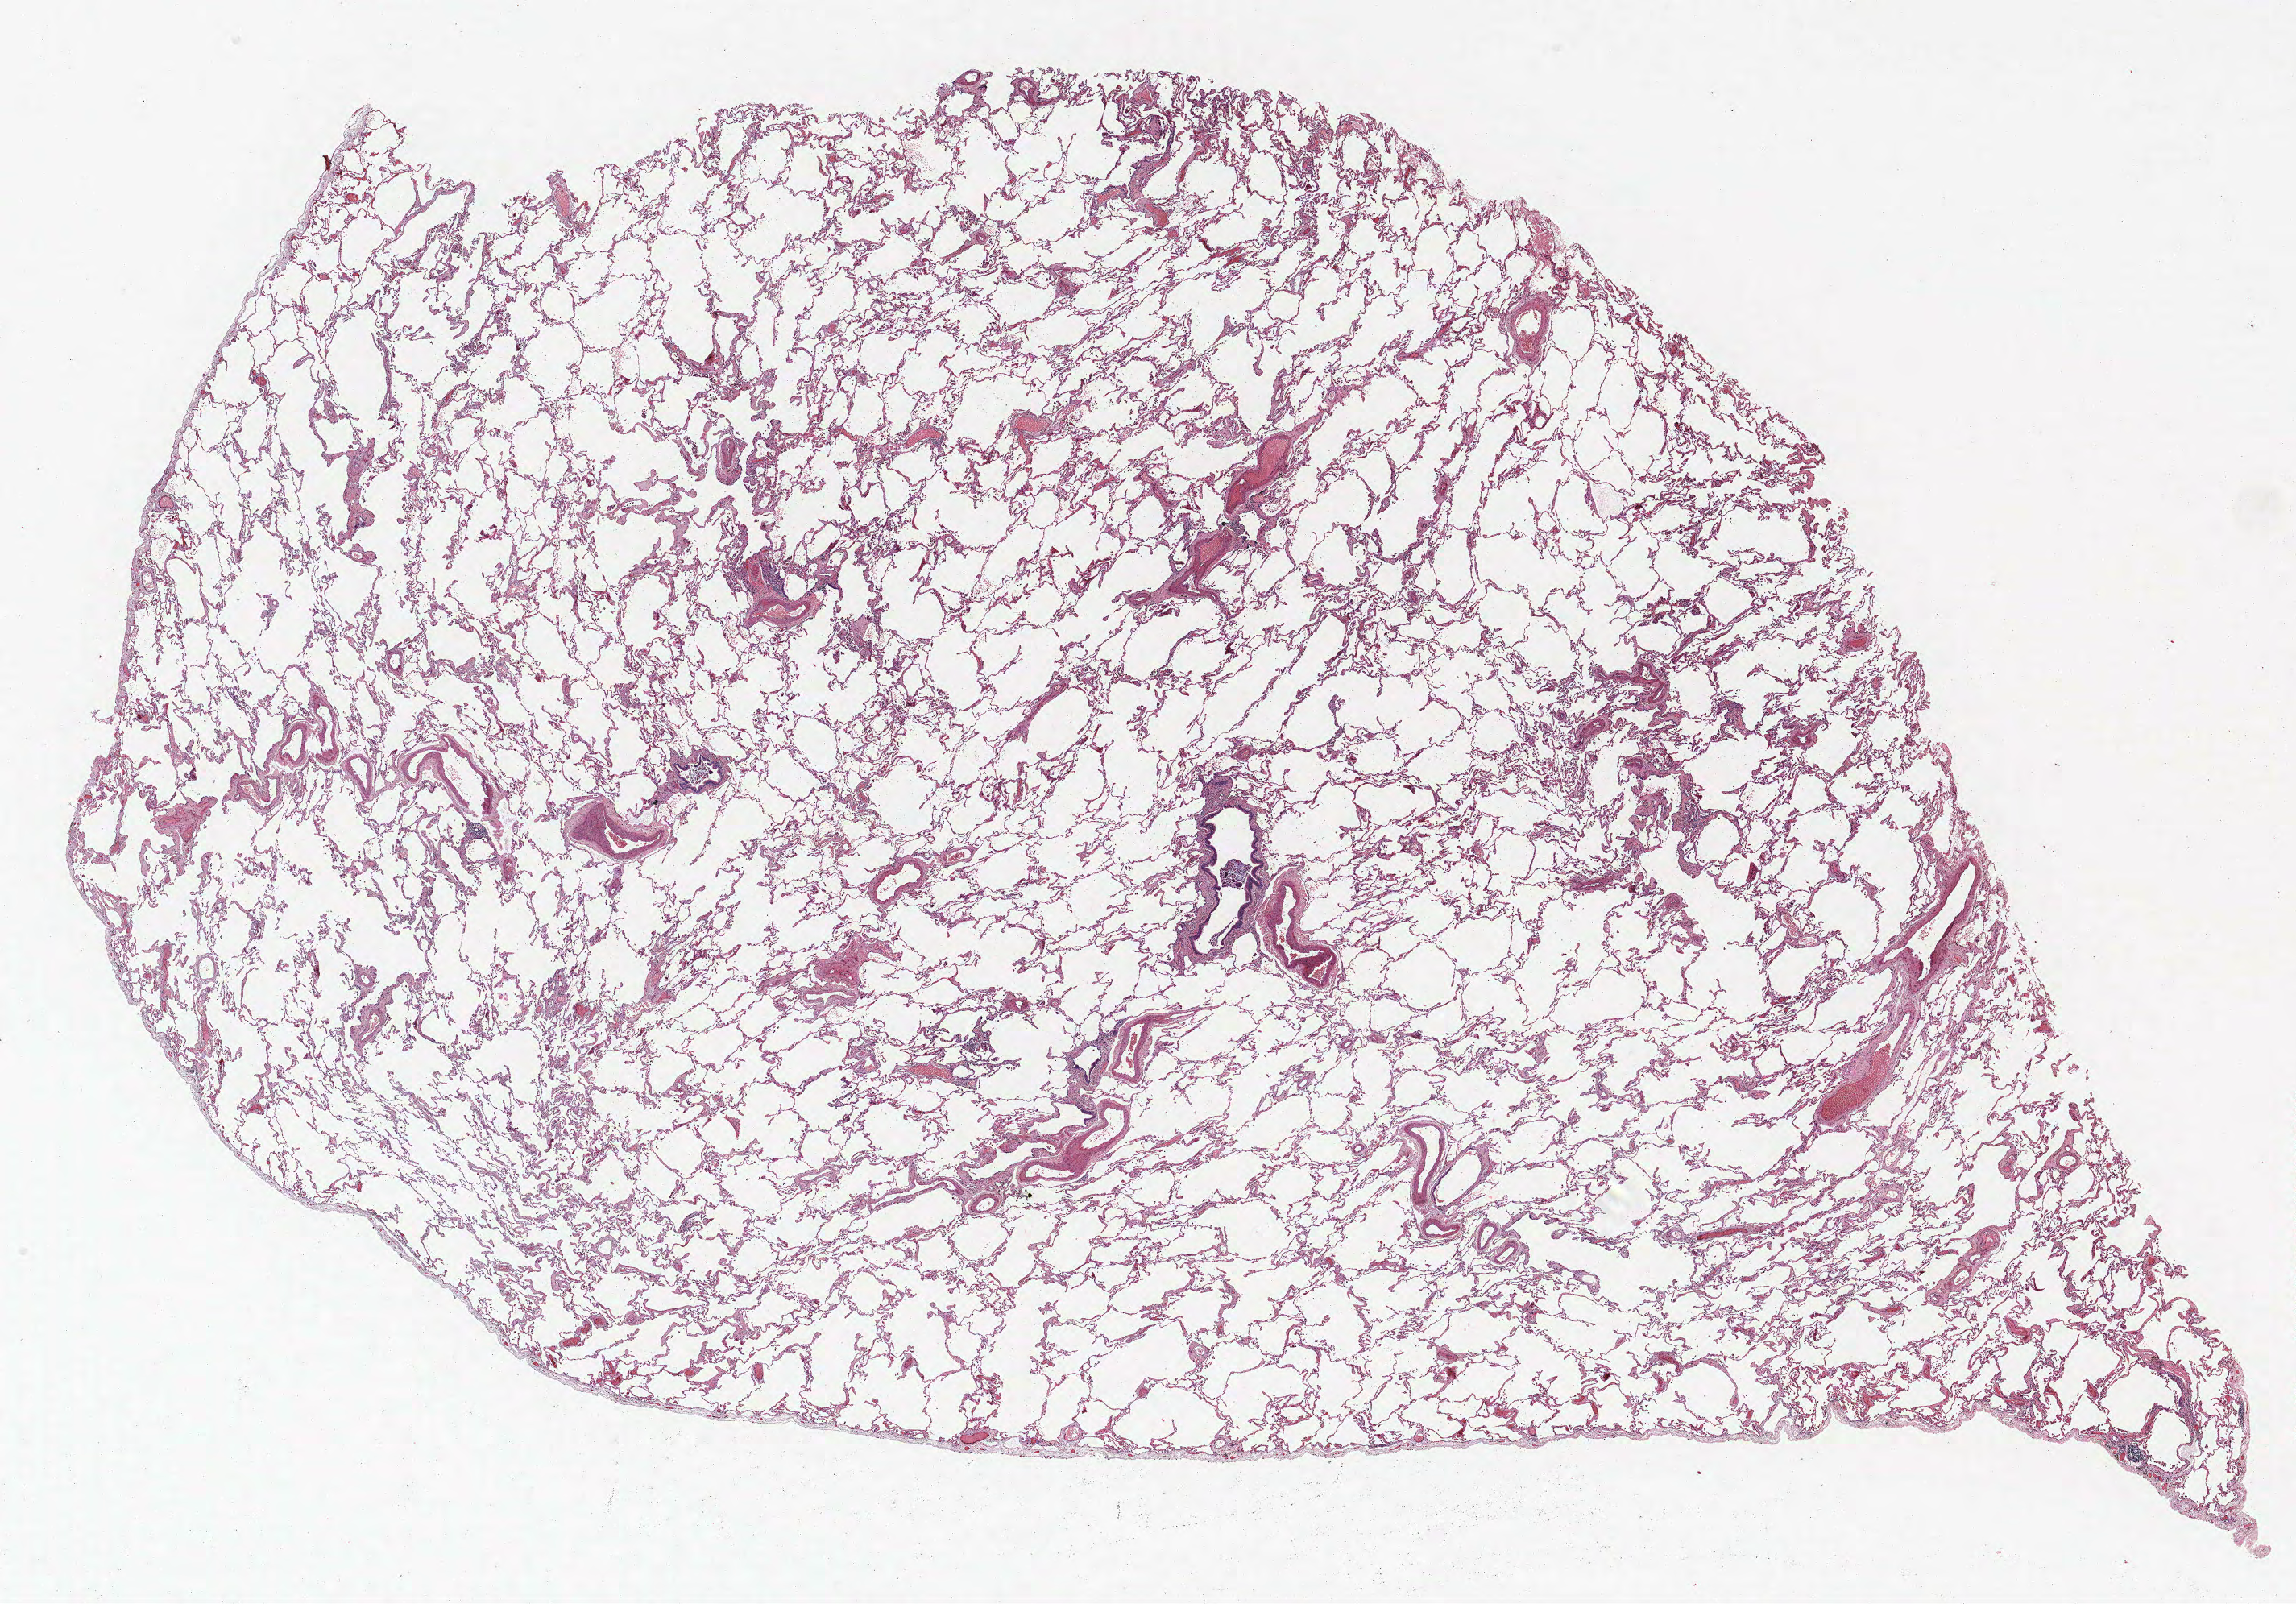
Whole-slide histology image, H&E-stained — shown as a low-resolution overview of the whole scanned area (about 22.8 x 15.9 mm), formalin-fixed paraffin-embedded (FFPE) section, lung tissue. Female, age 71 at enrolment. Current smoker at enrolment. Grade: moderately differentiated (G2).
Primary tumour location (clinical record): right middle lobe. Stage (AJCC 6th edition): IA. Tumour size (pathology): 12 mm. Participant's lung-cancer diagnosis: Adenocarcinoma, NOS.